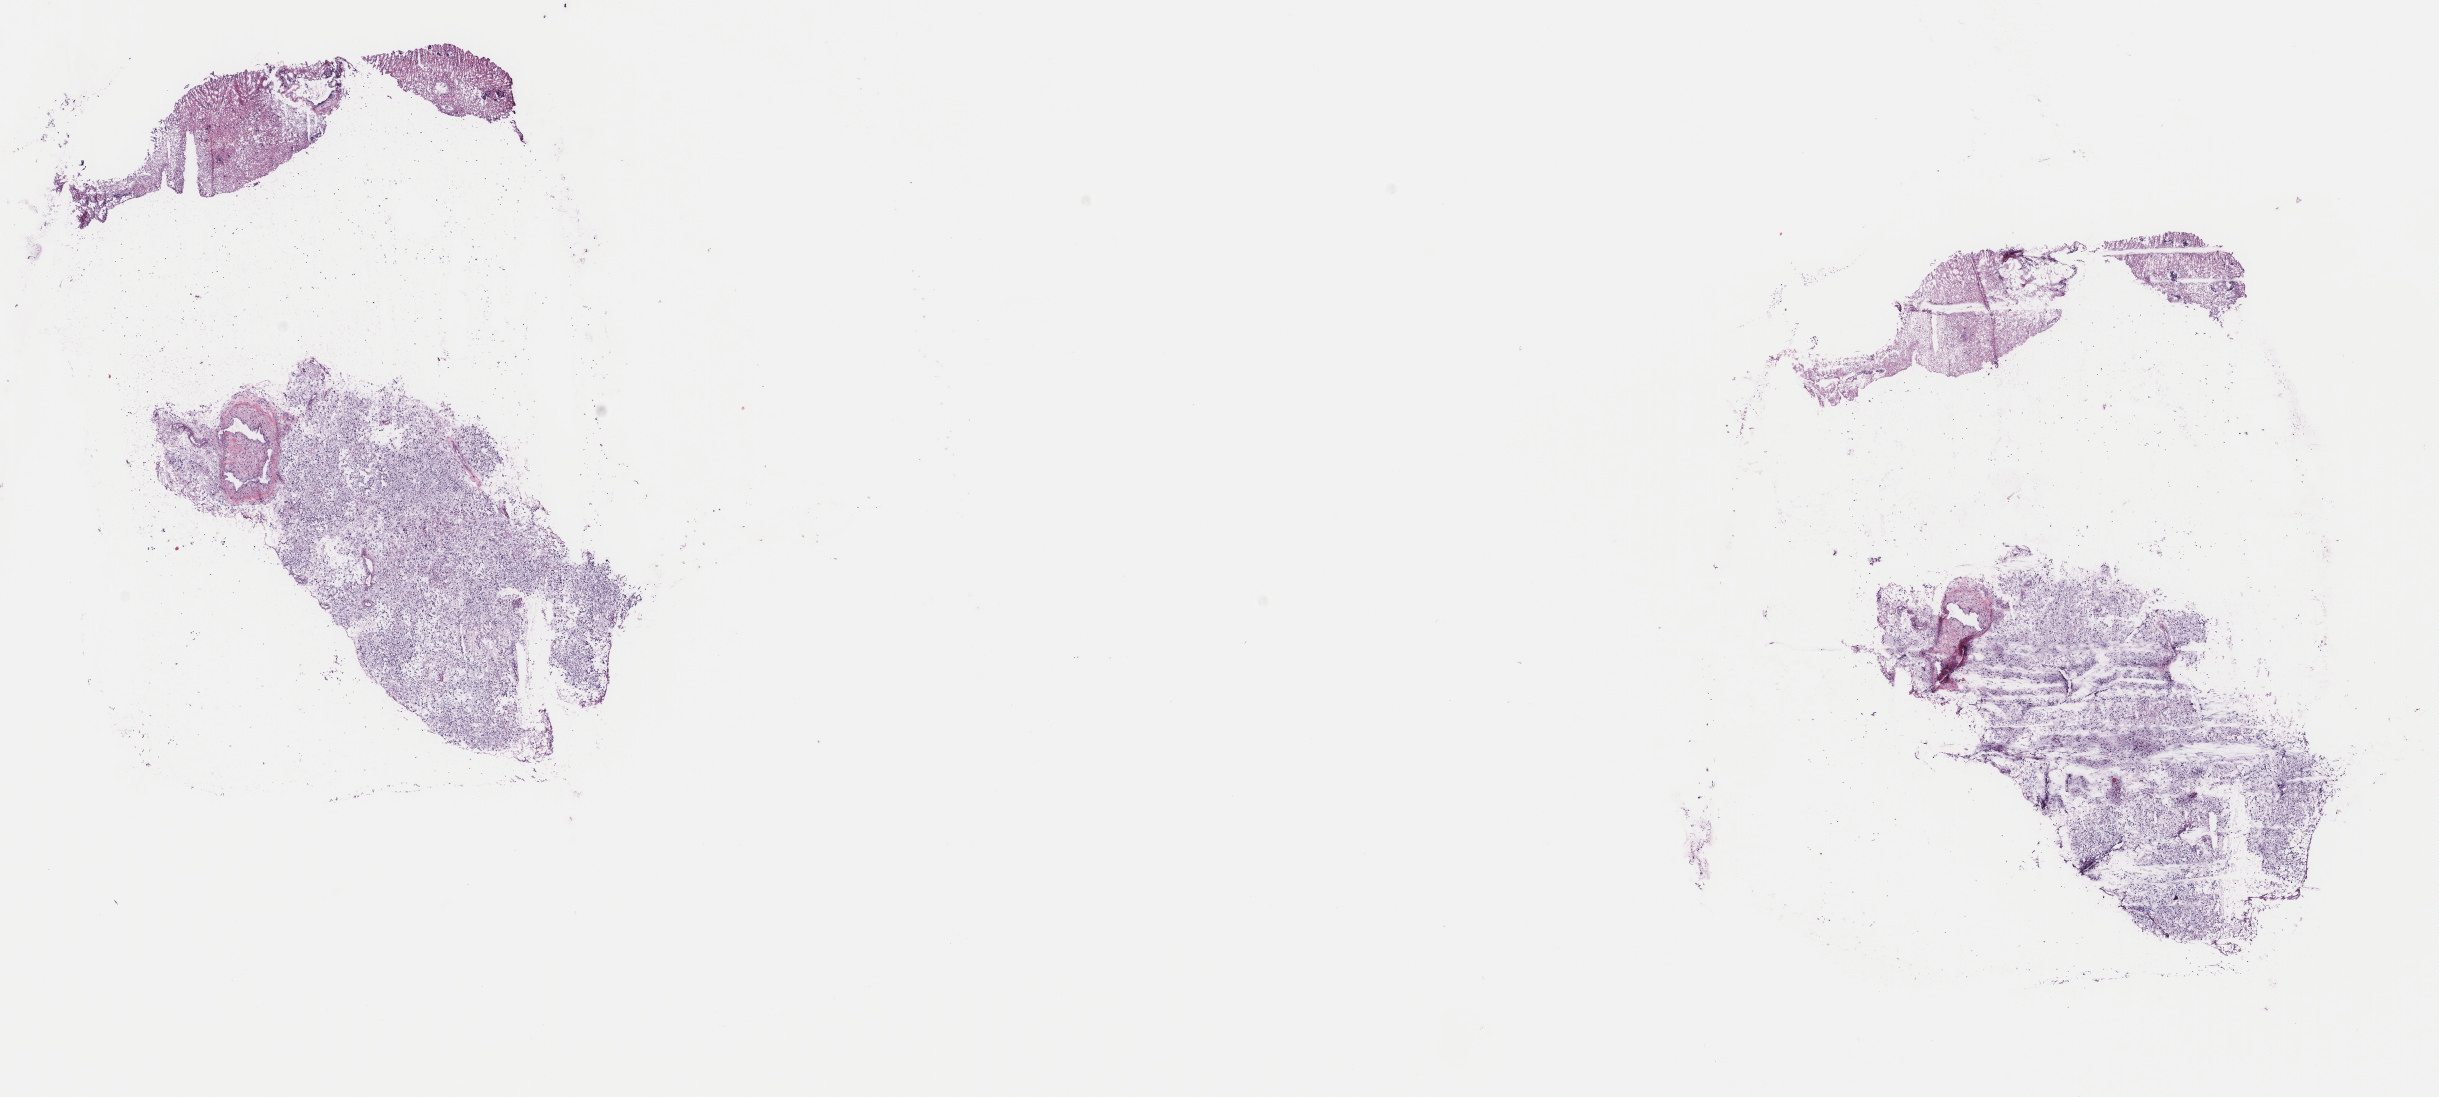
Whole-slide histology image, H&E-stained — whole scanned area (about 19.4 x 8.7 mm, from a 40x scan) shown as a low-resolution overview; frozen section from the top of the tissue portion; primary tumour sample from the brain. Patient: male, age at initial diagnosis 54 years. Histologic grade: G3 (poorly differentiated). Slide review estimates, as recorded: tumour cells 75%, tumour nuclei 90%, normal cells 0%, stromal cells 25%, necrosis 0%. Infiltration values recorded for this section: lymphocyte infiltration 0%, monocyte infiltration 0%, neutrophil infiltration 0%.
* diagnosis: Oligodendroglioma, anaplastic